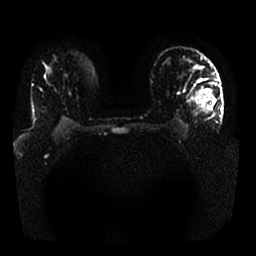
Breast MRI, one axial slice. Slice 19 of 25 in the series (ordered by position). Diffusion-weighted series; image 2 of 4 stored at this slice position (different b-values; order by instance number). 1.5 T. 256 × 256 image matrix, field of view 340 × 340 mm. Female patient.
Outlined on this slice (manually delineated by an expert):
- tumour on diffusion-weighted imaging: bounding box [x1, y1, x2, y2] px = [198, 89, 216, 108]